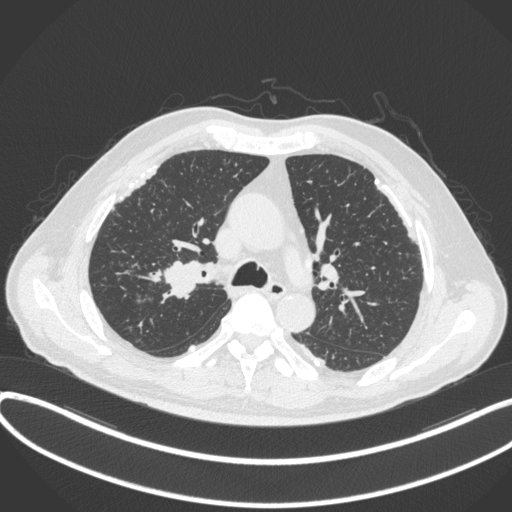
Chest CT, one axial slice; slice 284 of 455 in the series (ordered by position); reconstruction kernel B31f; 120 kVp; lung window (W 1500 / L -600 HU); 1 mm slice thickness; 512 × 512 image matrix. Male patient, age 58 years. From the clinical record (not read from this slice): clinical TNM (as recorded): T1c N0 M0.
Structures marked on this image (bounding box drawn by a radiologist):
- lung tumour (recorded histology: squamous cell carcinoma): bounding box <159,254,204,300> (left, top, right, bottom; pixels)